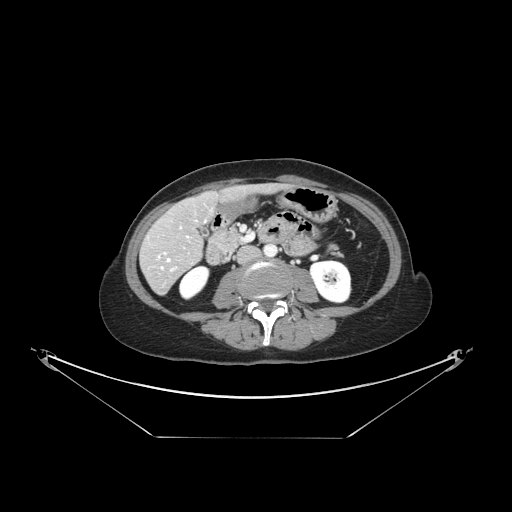
Contrast-enhanced abdominal CT, one axial slice; slice 47 of 148 in the series (ordered by position); 120 kVp; intravenous contrast given; soft-tissue window (W 400 / L 40 HU); 2.5 mm slice thickness; 512 × 512 image matrix, field of view 500 × 500 mm. Female patient, age 73 years. Case-level facts recorded for this patient, not image findings: diagnosis: colorectal cancer liver metastases, imaged before liver resection; multiple liver metastases: no; largest metastasis: 1 cm; chemotherapy before resection: yes.
Annotated regions visible in this slice (manually delineated by an expert):
- hepatic veins: box from (x=158, y=227) to (x=189, y=271) px
- liver: (x=143, y=187)–(x=271, y=293)
- planned liver remnant (the part of the liver to remain after resection): (x=162, y=187)–(x=264, y=244)